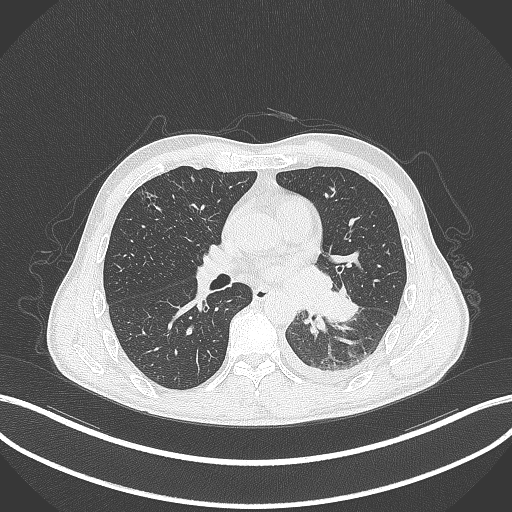
Chest CT, one axial slice; slice 163 of 295 in the series (ordered by position); reconstruction kernel B70f; lung window (W 1500 / L -600 HU); 512 × 512 image matrix, field of view 400 × 400 mm. Male patient, age 47 years. From the clinical record (not read from this slice): clinical TNM (as recorded): T3 N1 M1c; histopathological grade: G3.
Annotated regions visible in this slice (rectangle marked by the reading radiologist):
- lung tumour (recorded histology: small cell carcinoma): bounding box (x1, y1, x2, y2) in pixels: (317, 284, 364, 325)